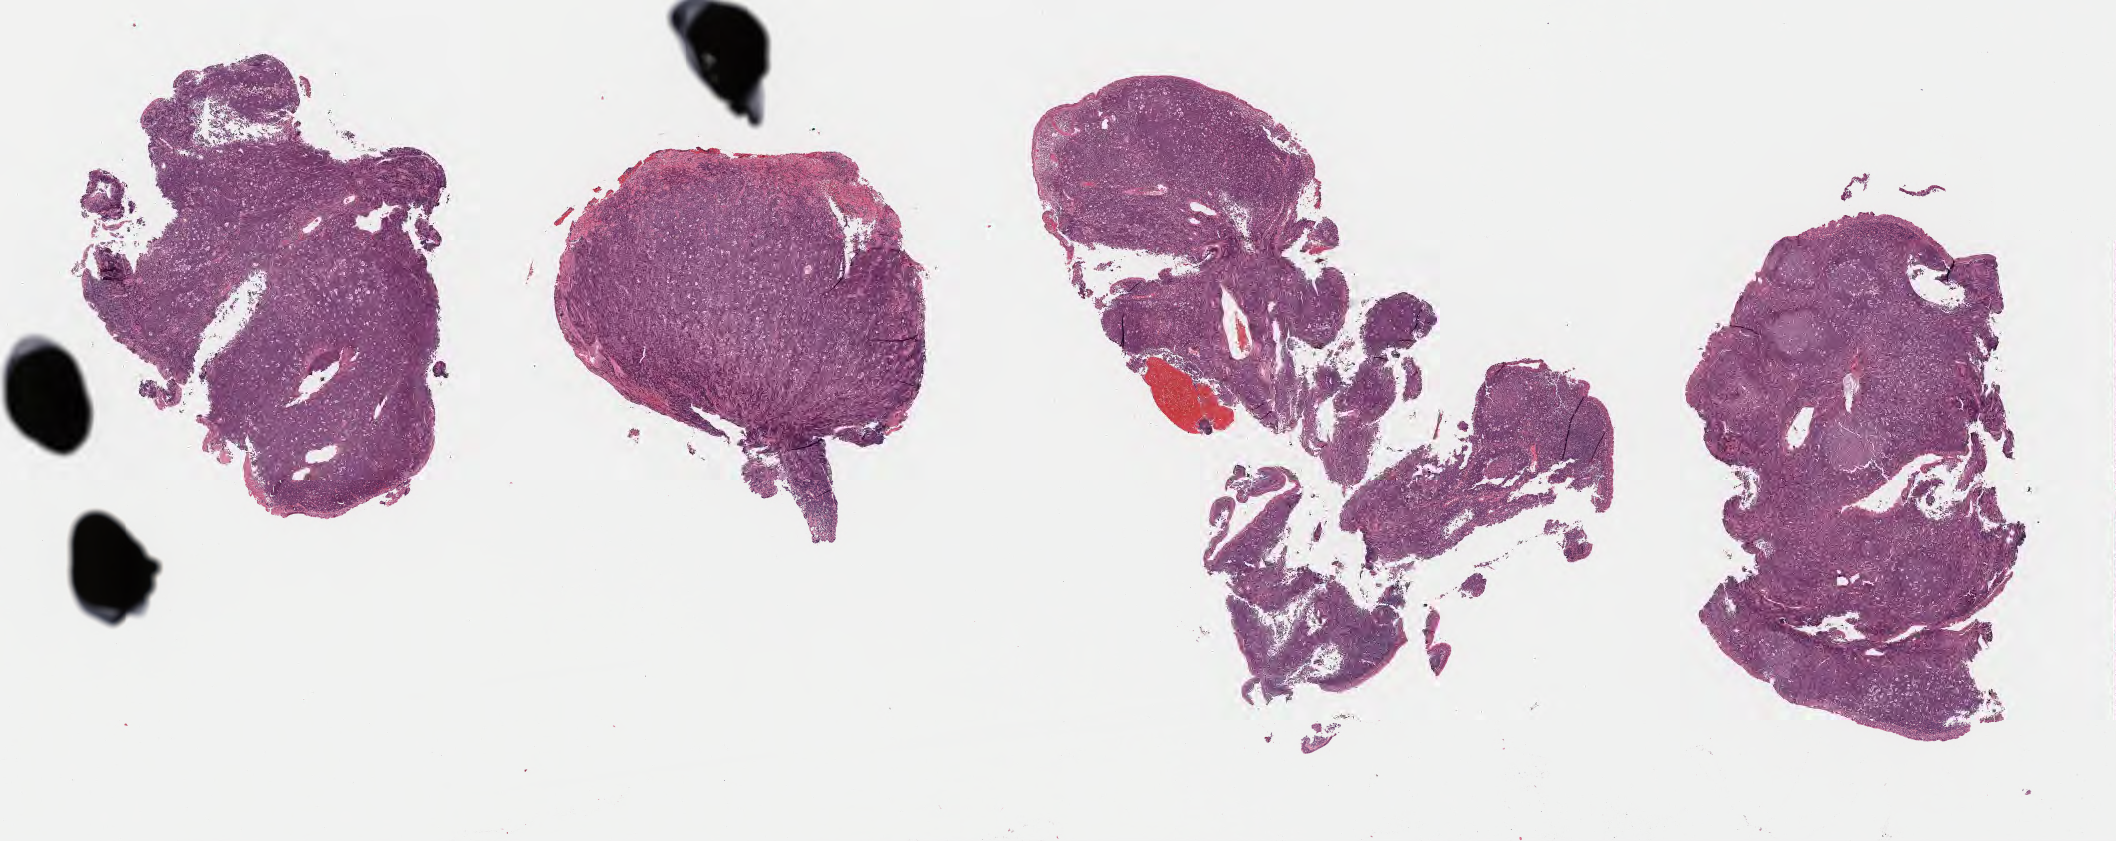
Whole-slide image, hematoxylin and eosin (H&E) stain — low-resolution overview of the scanned area, about 17.1 x 6.8 mm; tumor tissue. Patient: male, age at initial diagnosis 5 years.
Diagnosis: Burkitt lymphoma, NOS.